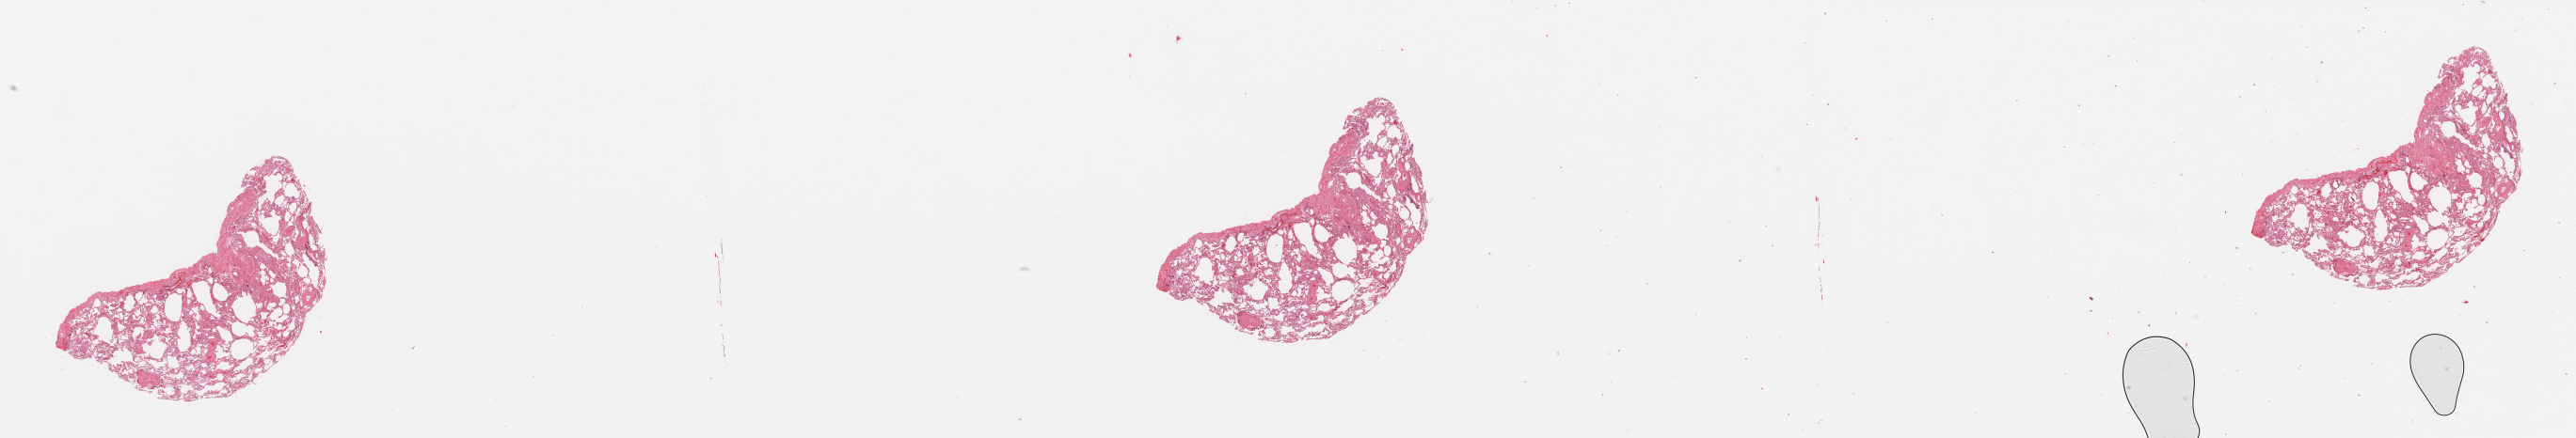
Digitized H&E tissue section (whole slide), a low-resolution overview of the entire scanned area, about 43.3 x 7.4 mm (from a 20x scan); lung, normal (non-tumour) tissue. Patient: male, age 81 years.
This section: normal (non-tumour) tissue from the same patient. Patient diagnosis: Adenocarcinoma, NOS.